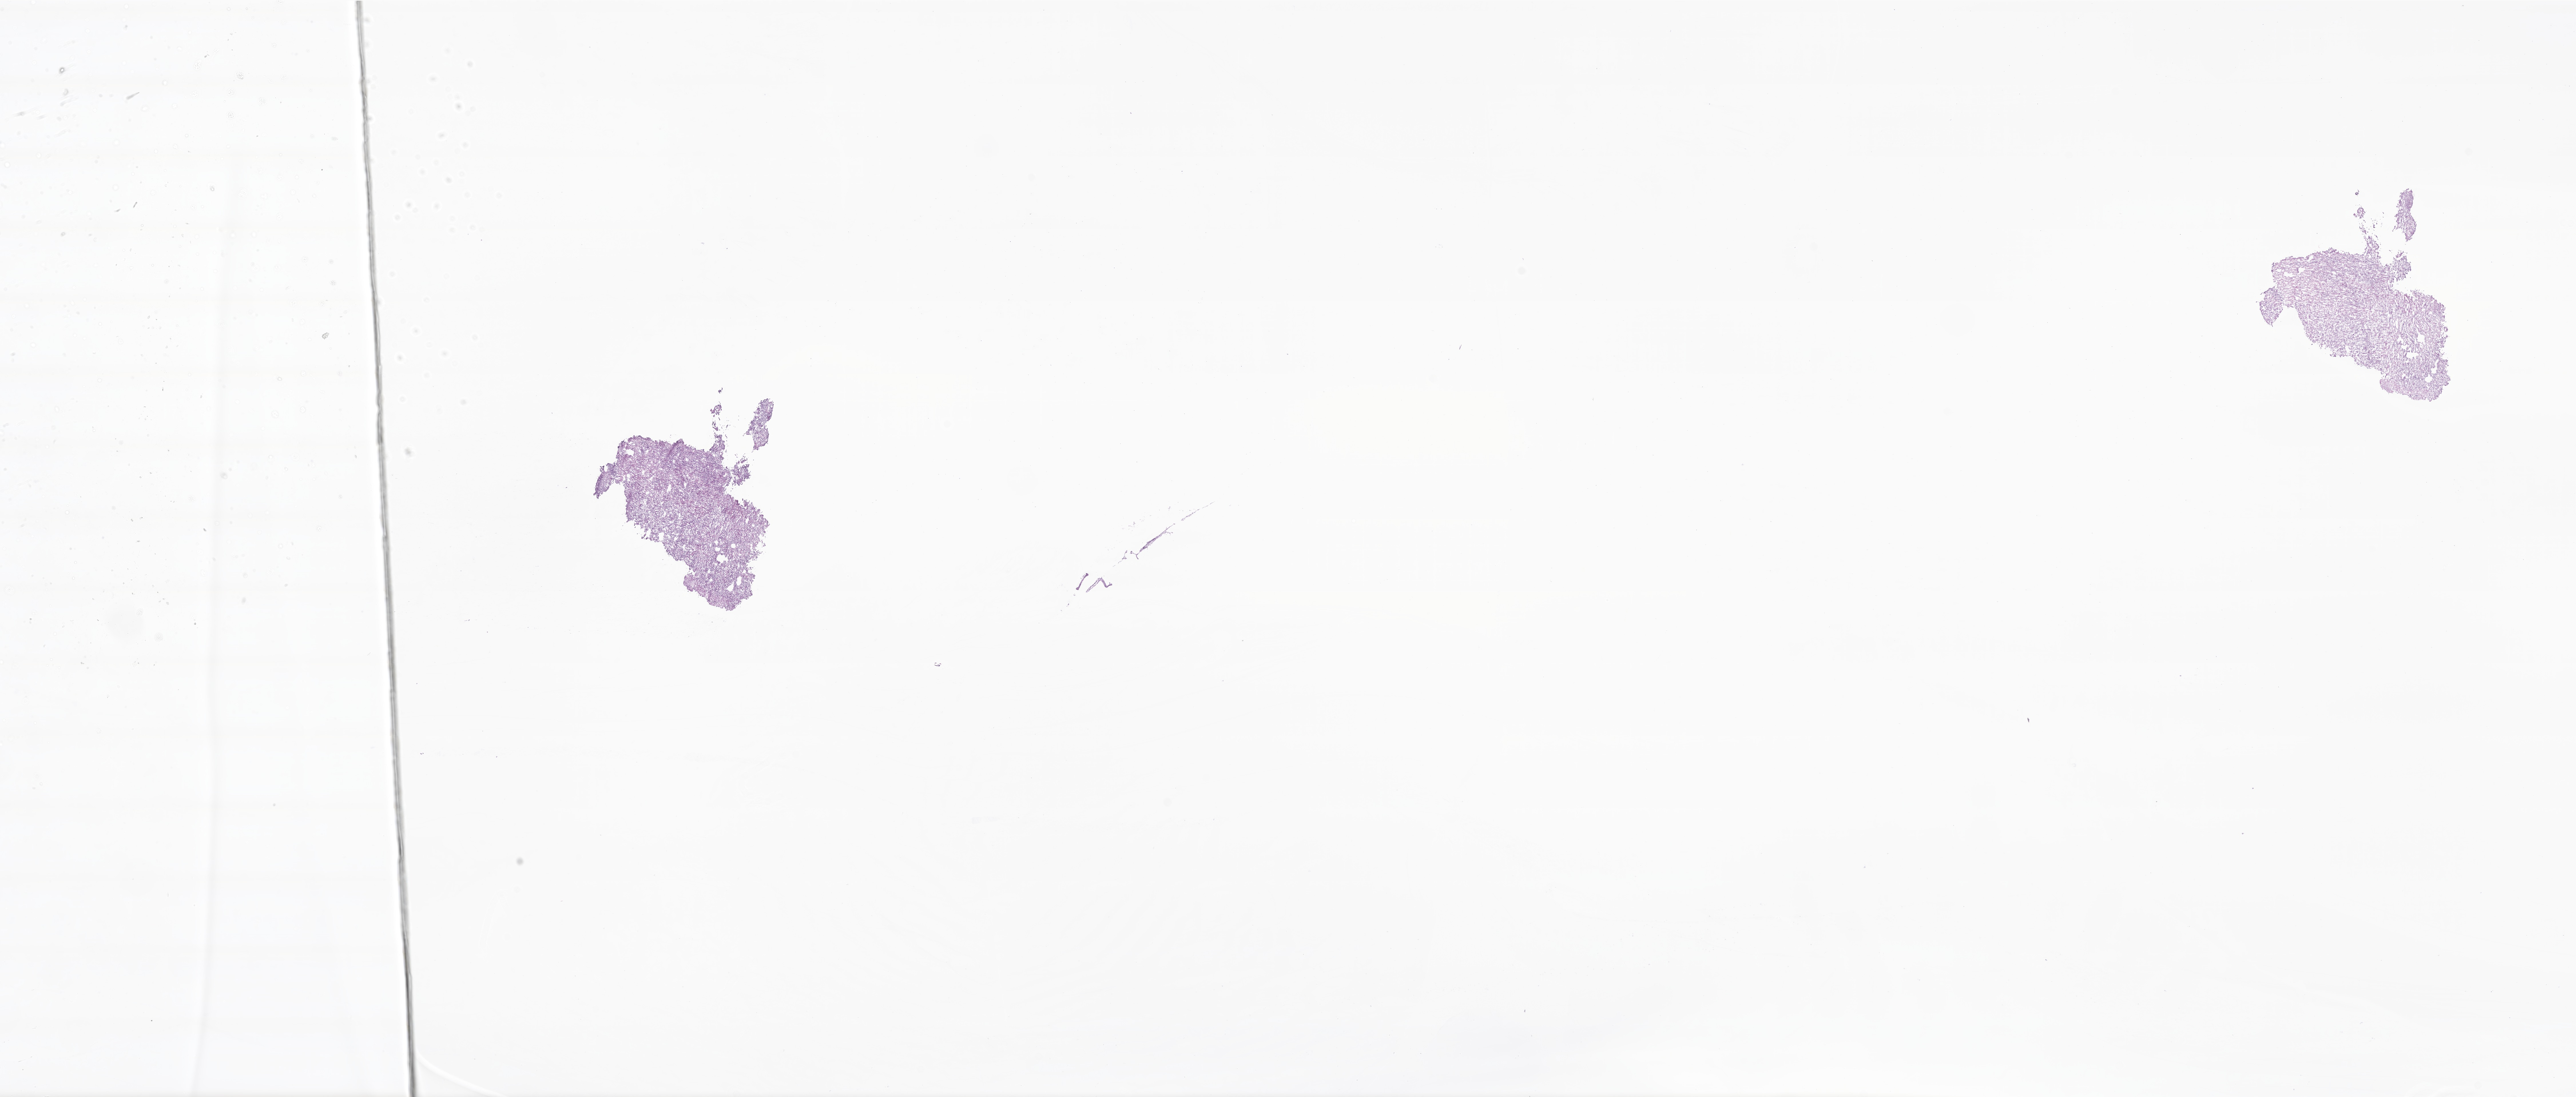
Whole-slide image, hematoxylin and eosin (H&E) stain of tumor tissue from the brain — low-resolution overview of the scanned area, about 38.0 x 16.2 mm. Frozen section. Patient male; age 170 months (14 years 2 months).
Diagnosis: Medulloblastoma, NOS.